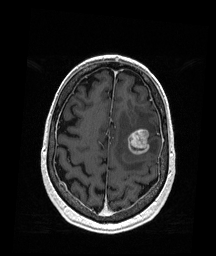
Brain MRI from a brain-tumour surgery series, one axial slice. Position 53 of 176 along the scan axis. T1-weighted post-contrast. 216 × 256 image matrix, field of view 211 × 250 mm. From the clinical record (not read from this slice): histopathology: Metastatic Melanoma; tumour location: Left Frontal.
Annotated regions visible in this slice (expert manual segmentation):
- tumour: bounding box (x1, y1, x2, y2) in pixels: (127, 129, 150, 156)